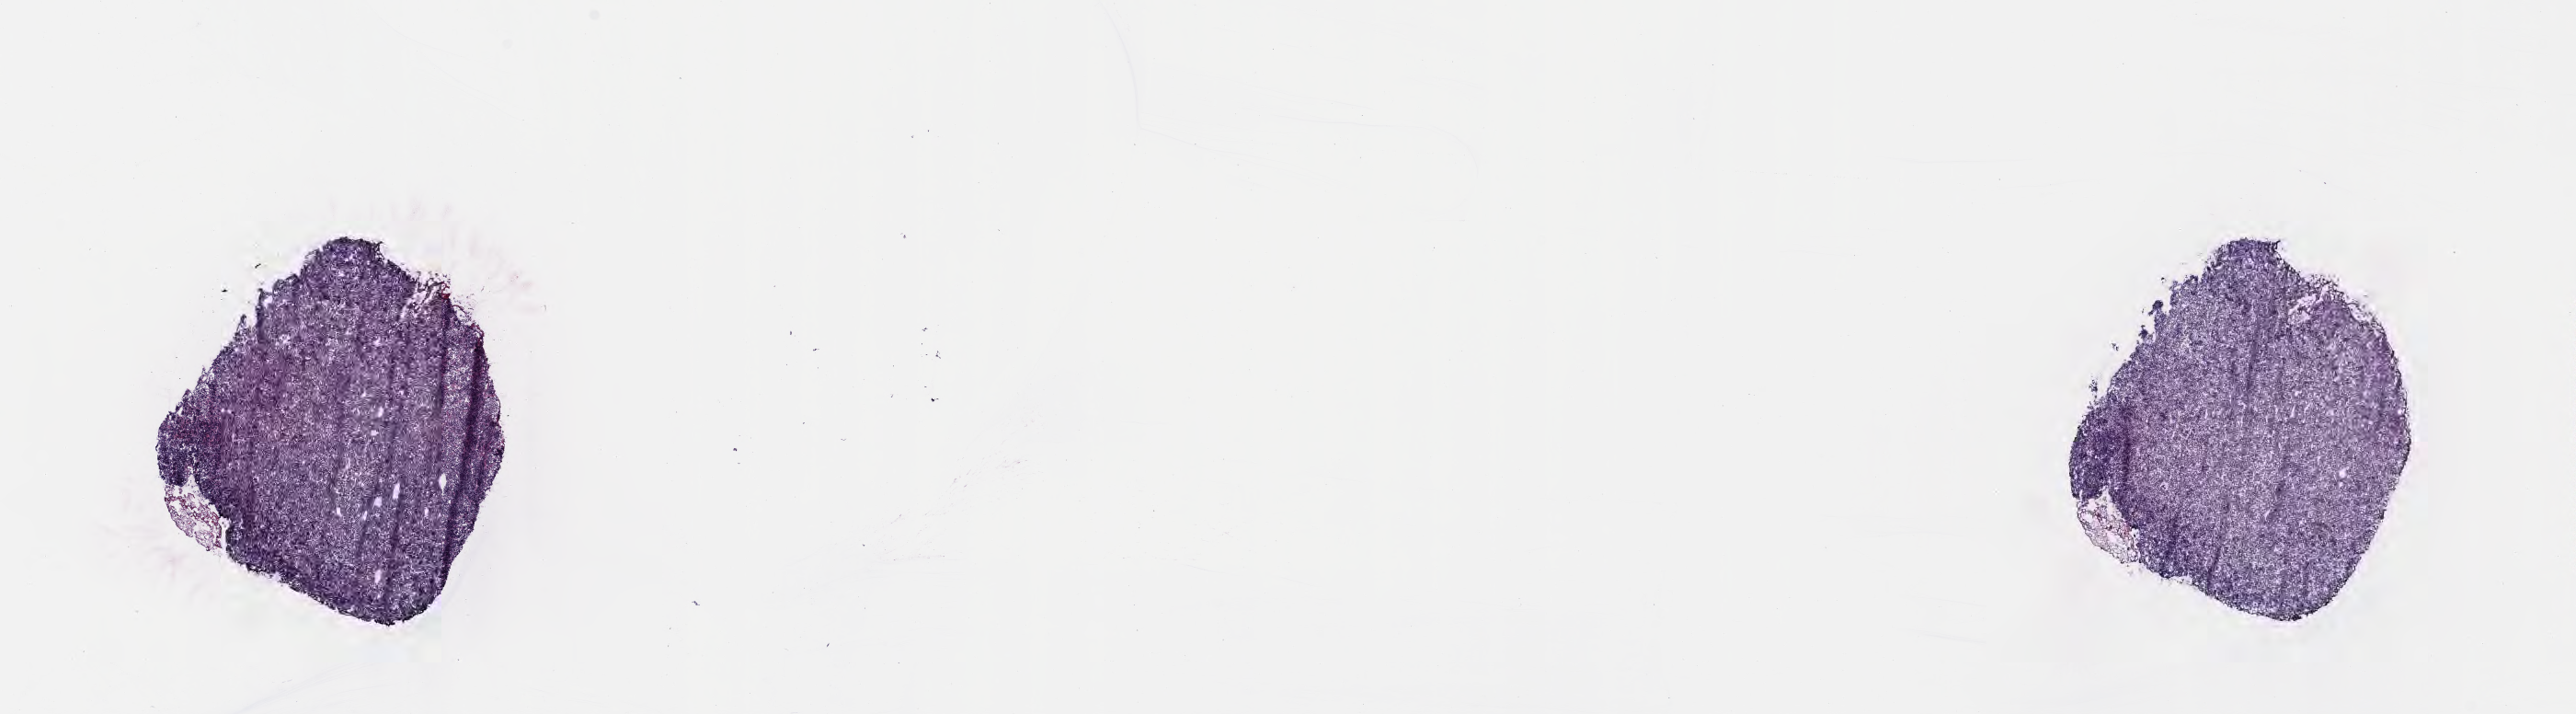
Haematoxylin and eosin whole-slide image — whole scanned area (about 22.6 x 6.3 mm) shown as a low-resolution overview. Frozen section. Specimen: primary tumor. Site: cranium. Male, age 6 years at initial diagnosis. Pathologist review of this section (percent, as recorded): tumor cells 95%, tumor nuclei 90%, stromal cells 0%, necrosis 5%, normal cells 0%. Infiltration values recorded for this section: lymphocyte infiltration 40%, monocyte infiltration 20%, neutrophil infiltration 5%.
• Ann Arbor stage (patient): Stage III
• diagnosis: Burkitt lymphoma, NOS